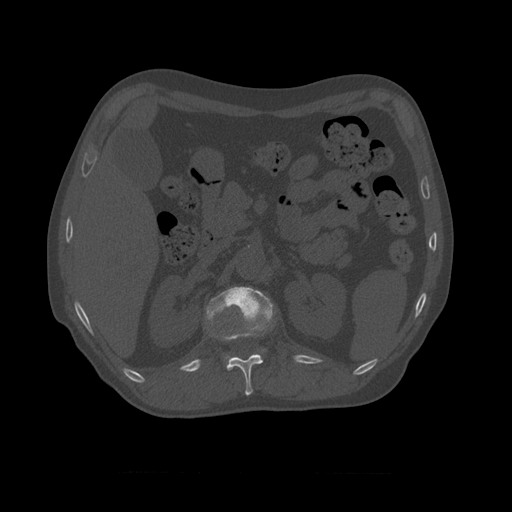
CT including the spine, one axial slice; slice 370 of 450 in the series (ordered by position); reconstruction kernel STANDARD; bone window (W 1800 / L 400 HU); 1.25 mm slice thickness; 512 × 512 image matrix, field of view 405 × 405 mm. Patient age 75 years. From the clinical record (not read from this slice): primary cancer: prostate.
Outlined on this slice (semi-automatic segmentation, software-assisted and operator-edited):
- L1 vertebra: box from (x=206, y=287) to (x=275, y=361) px
- T10 vertebra: (x=262, y=349)–(x=266, y=353)
- T11 vertebra: (x=210, y=331)–(x=264, y=396)